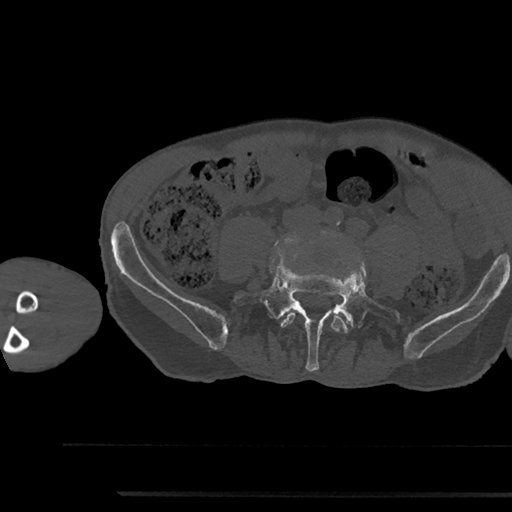
CT including the spine, one axial slice; slice 366 of 797 in the series (ordered by position); reconstruction kernel Br40s/3; 120 kVp; bone window (W 1800 / L 400 HU); 0.5 mm slice thickness; 512 × 512 image matrix, field of view 367 × 367 mm. Male patient, age 79 years. From the clinical record (not read from this slice): primary cancer: prostate.
Outlined on this slice (semi-automatic segmentation, software-assisted and operator-edited):
- L4 vertebra: box from (x=281, y=311) to (x=349, y=333) px
- L5 vertebra: (x=234, y=262)–(x=401, y=371)